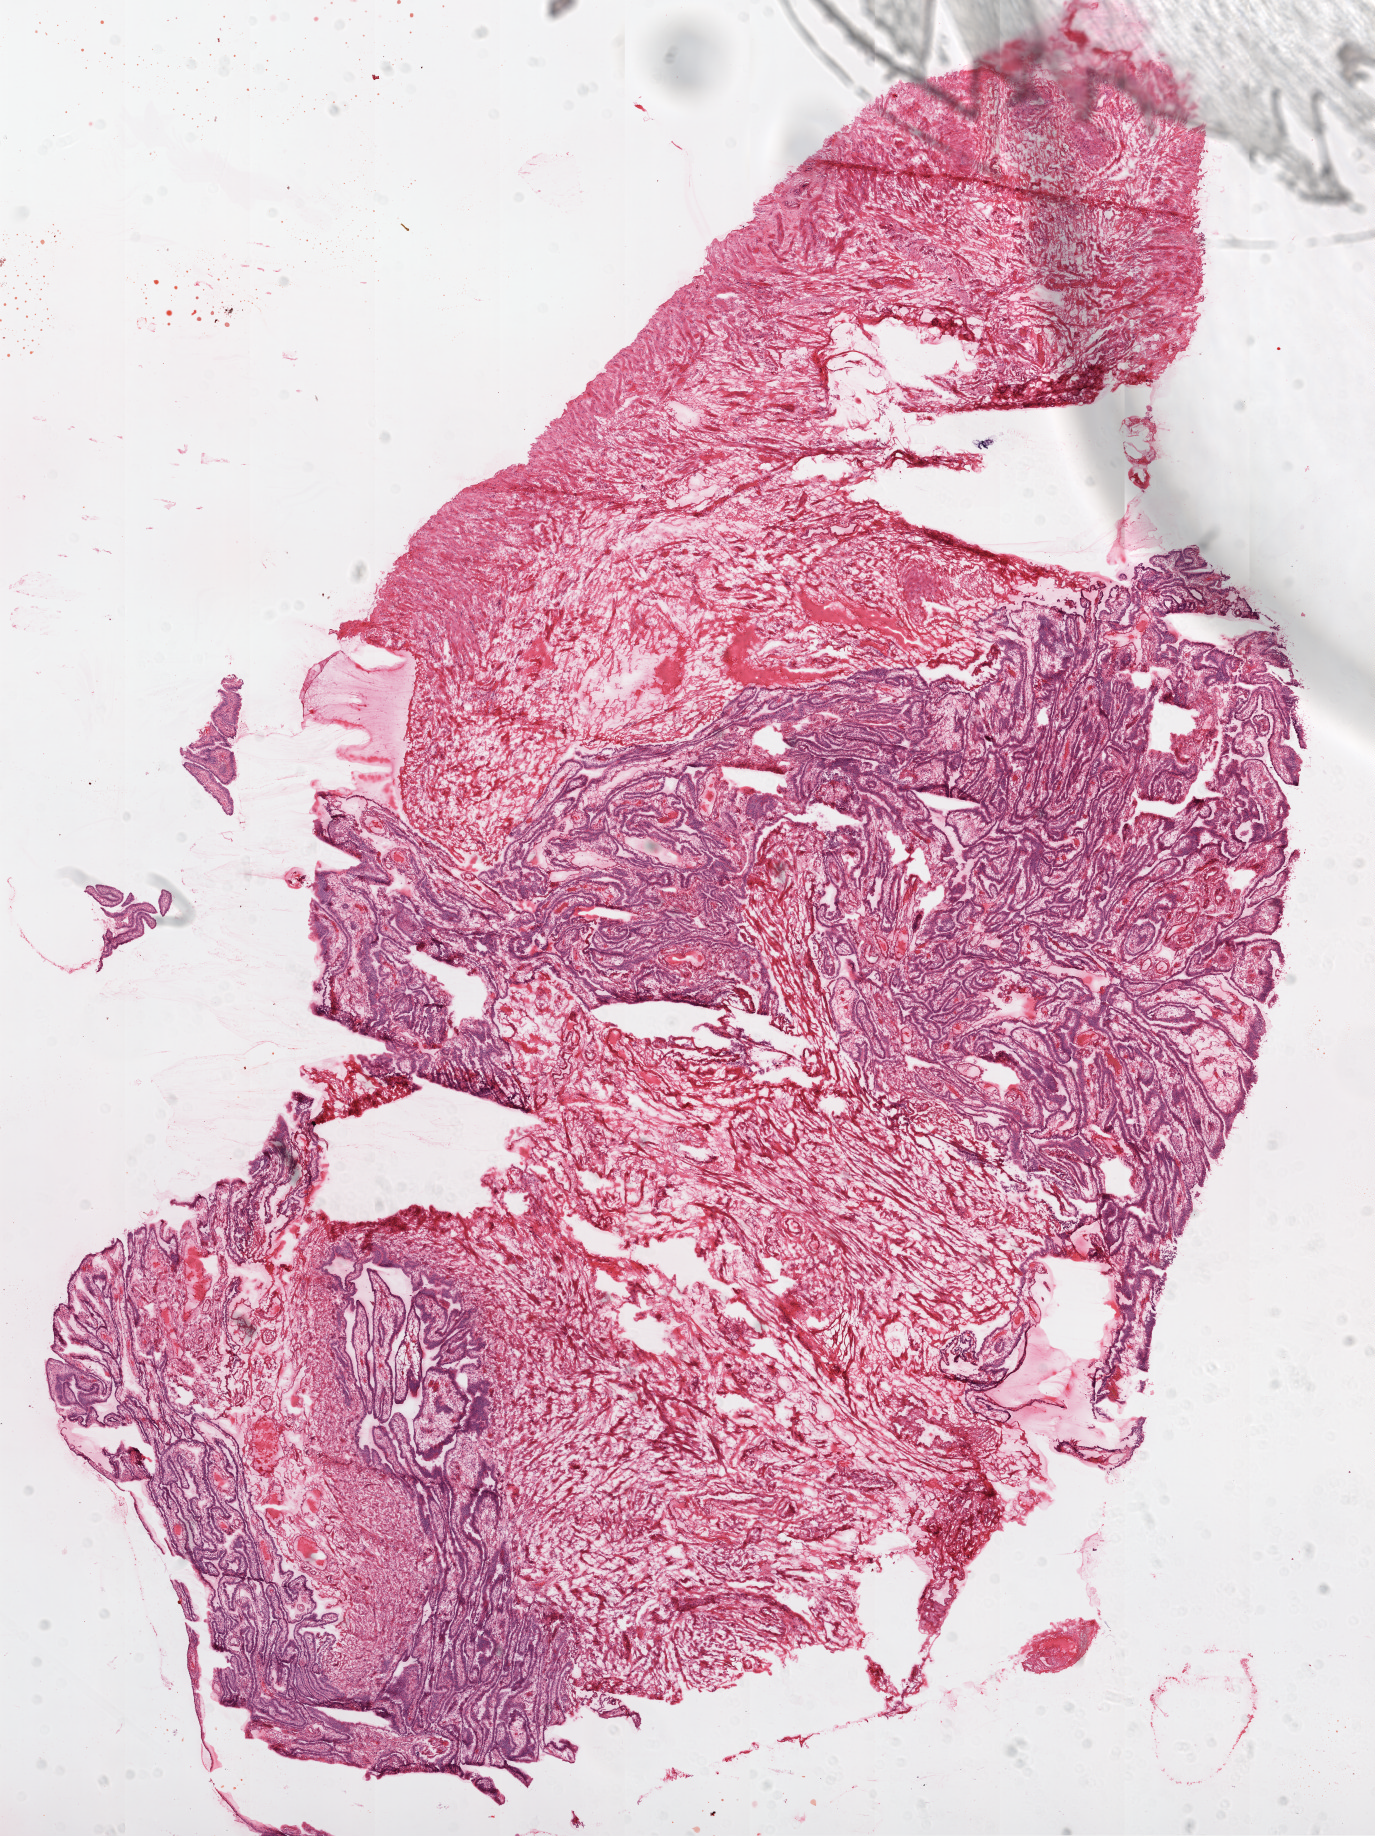
Whole-slide histology image, H&E-stained, low-resolution overview of the scanned area, about 11.0 x 14.7 mm; frozen section from the top of the tissue portion; solid tissue normal (non-tumour tissue) sample from the ovary. Female, age 52 years at initial diagnosis.
• this section: solid tissue normal sample (biorepository sample class)
• patient diagnosis: Serous cystadenocarcinoma, NOS